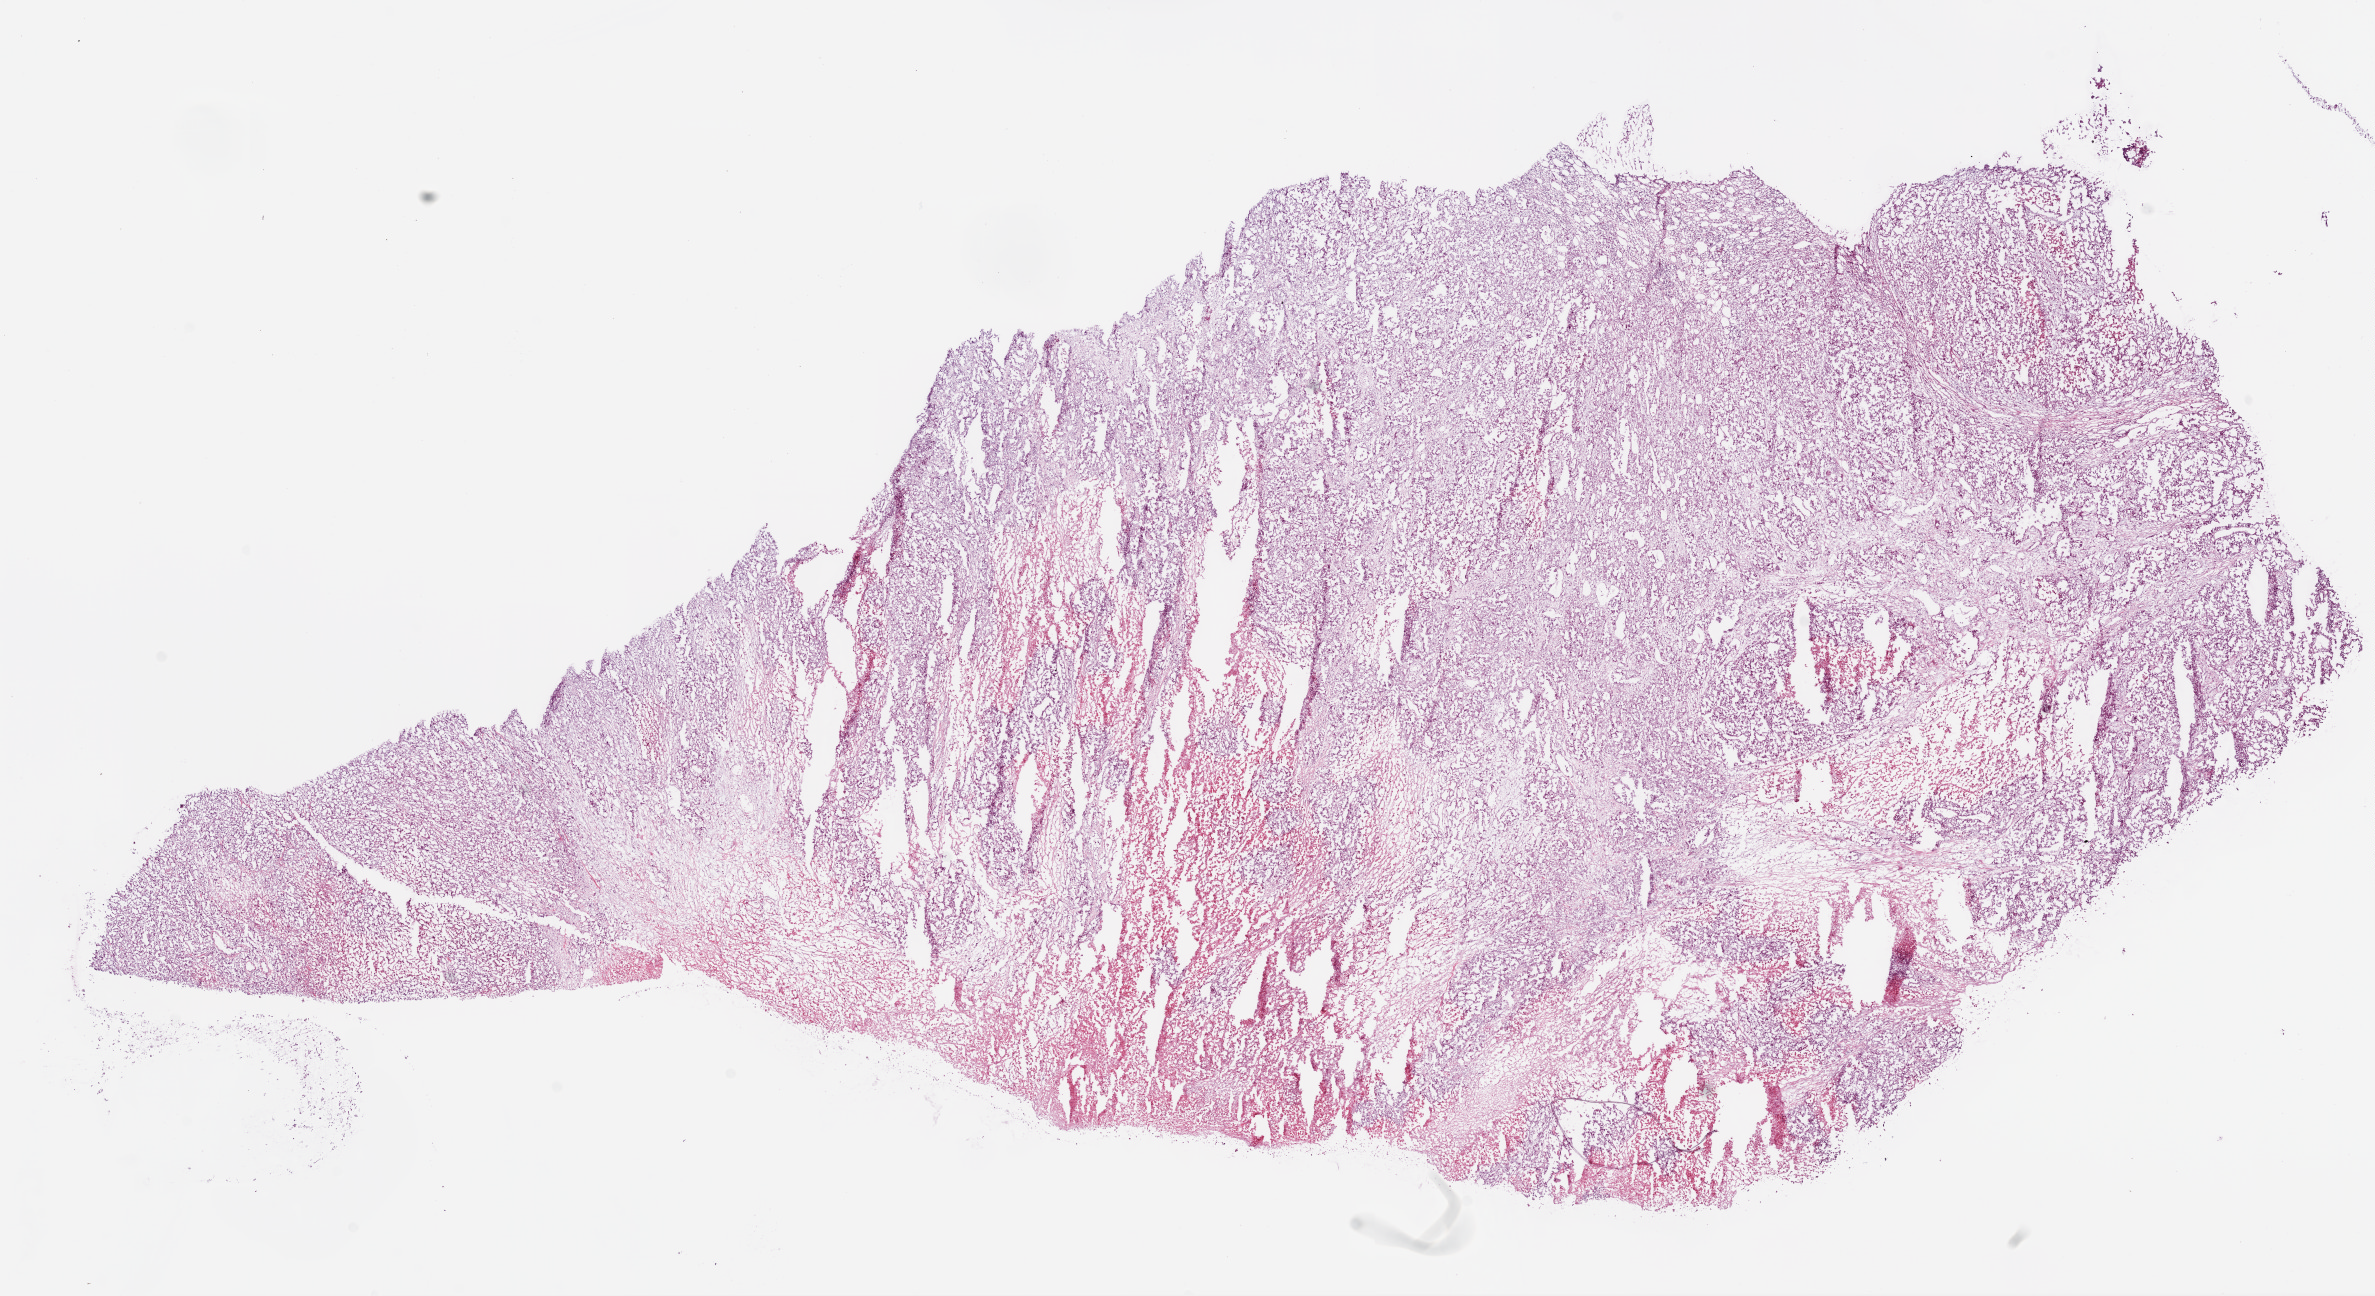
Digitized H&E tissue section (whole slide), low-resolution overview of the scanned area, about 19.1 x 10.4 mm, frozen section from the bottom of the tissue portion, primary tumour sample from the kidney. Female, age 53 years at initial diagnosis. Pathologist review of this section (percent, as recorded): tumour cells 70%, tumour nuclei 85%.
Diagnosis: Clear cell adenocarcinoma, NOS.